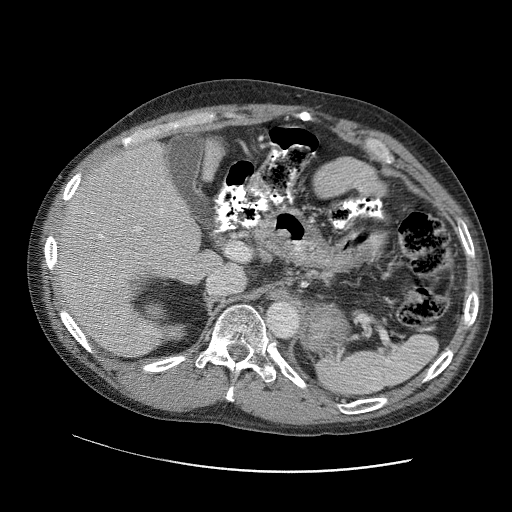
Contrast-enhanced abdominal CT (liver protocol), one axial slice. Position 65 of 109 along the scan axis. Reconstruction kernel STANDARD. 120 kVp. Soft-tissue window (W 400 / L 40 HU). 2.5 mm slice thickness. 512 × 512 image matrix, field of view 400 × 400 mm. From the clinical record (not read from this slice): diagnosis: hepatocellular carcinoma (patient treated with transarterial chemoembolisation; whether this scan precedes or follows treatment is not stated here); TNM stage (as recorded): Stage-IIIC; Child-Pugh class: B.
Structures marked on this image (semi-automatically segmented with operator editing):
- liver parenchyma outside the tumour (the mass and vessels are separate outlines, so this box may not span the whole liver): bounding box <54,140,200,356> (left, top, right, bottom; pixels)
- mass: <168,326,183,338>
- liver vessels: <54,169,190,338>